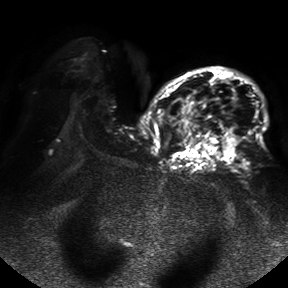
Breast MRI, one axial slice. Diffusion-weighted series; image 2 of 4 stored at this slice position (different b-values; order by instance number). 1.5 T. 4 mm slice thickness. 288 × 288 image matrix. Female patient.
Outlined on this slice (manually delineated by an expert):
- tumour on diffusion-weighted imaging: box from (x=183, y=98) to (x=239, y=158) px